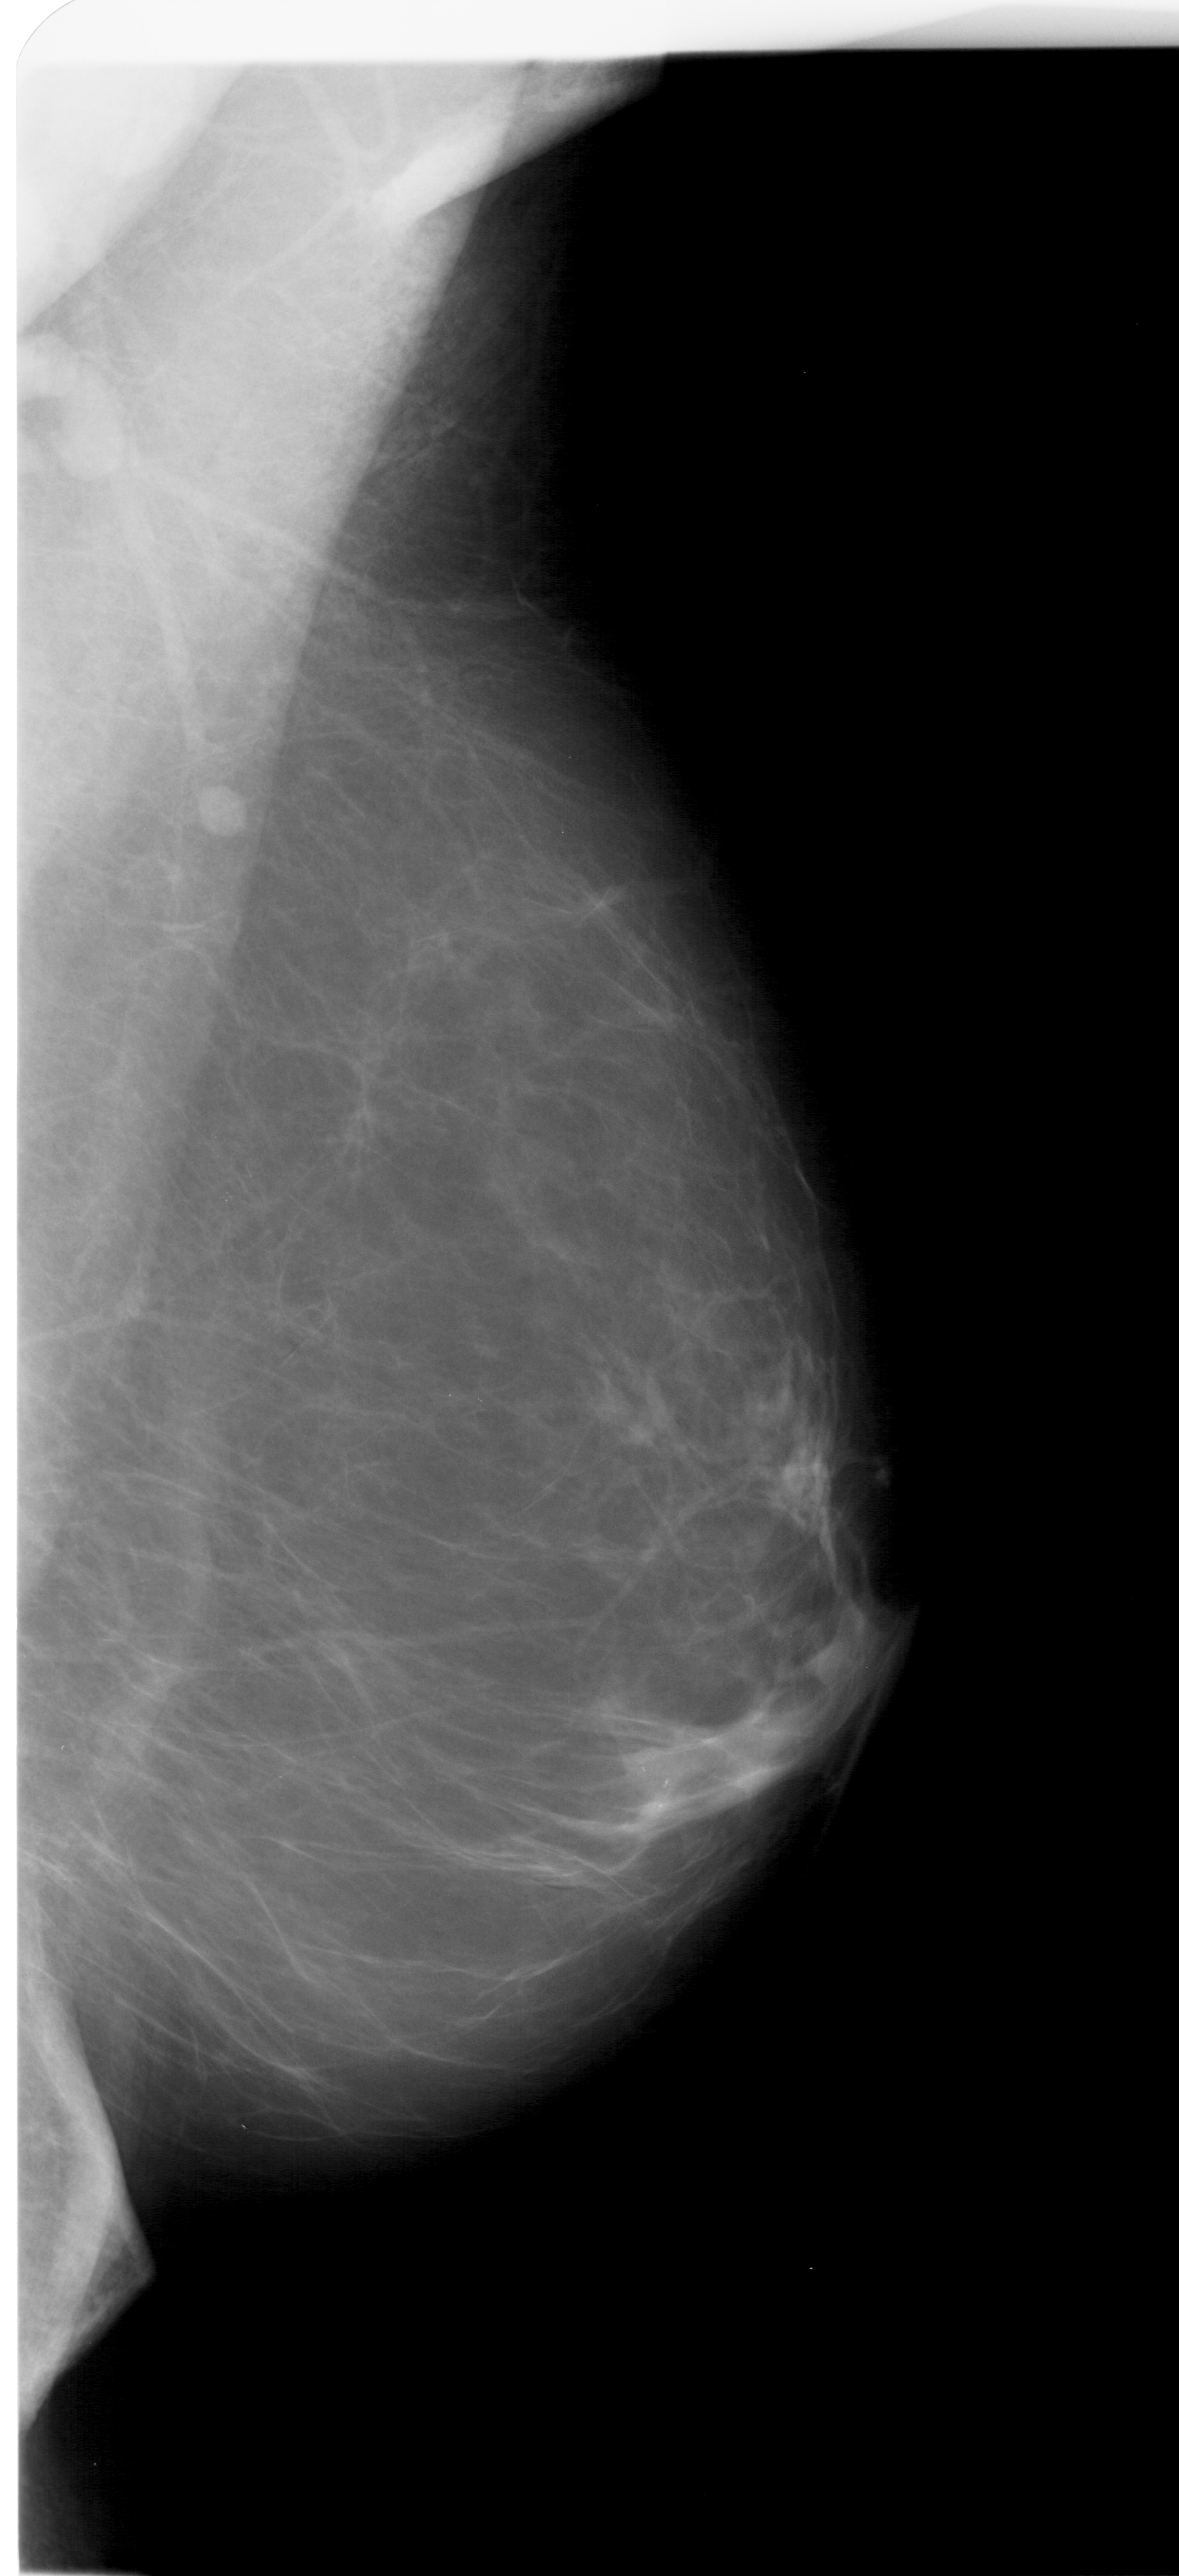
Mammogram (digitized film). Right breast. MLO view. BI-RADS breast density category 1 (scale 1–4). 1179 × 2576 image matrix.
Marked abnormalities (boxes around the expert regions of interest):
- calcifications, morphology pleomorphic, distribution clustered; BI-RADS assessment category 4; subtlety rating 3 on a 1 (subtle) to 5 (obvious) scale; pathology (as recorded): malignant: bounding box [x1, y1, x2, y2] px = [614, 1746, 691, 1845]